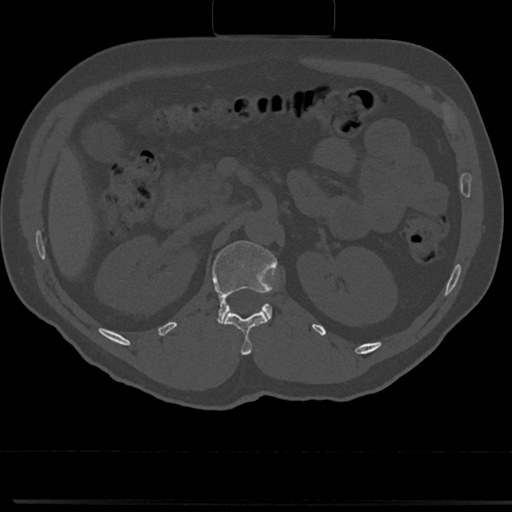
CT including the spine, one axial slice. Position 109 of 817 along the scan axis. Reconstruction kernel Br40s/3. 120 kVp. Bone window (W 1800 / L 400 HU). 0.5 mm slice thickness. 512 × 512 image matrix. Patient: male, 61 years. Case-level facts recorded for this patient, not image findings: primary cancer: prostate.
Annotated regions visible in this slice (semi-automatically segmented with operator editing):
- L1 vertebra: bounding box [x1, y1, x2, y2] px = [213, 240, 278, 326]
- T12 vertebra: [224, 311, 268, 354]